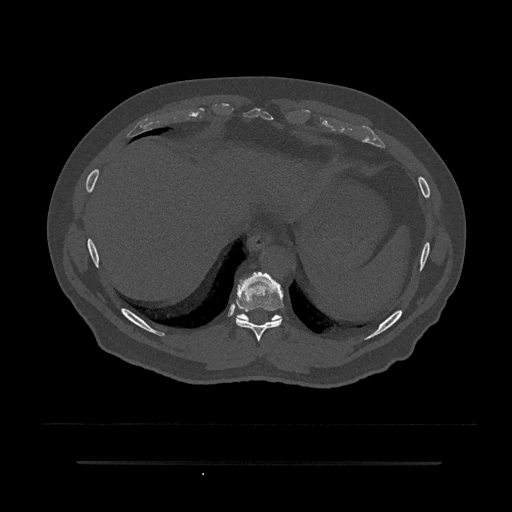
CT including the spine, one axial slice. Reconstruction kernel Br40s/3. Bone window (W 1800 / L 400 HU). 0.5 mm slice thickness. 512 × 512 image matrix, field of view 464 × 464 mm. Patient: male, 59 years. Case-level facts recorded for this patient, not image findings: primary cancer: bile ducts.
Structures marked on this image (semi-automatic segmentation, software-assisted and operator-edited):
- T10 vertebra: bounding box <237,314,280,327> (left, top, right, bottom; pixels)
- T9 vertebra: <236,272,284,341>